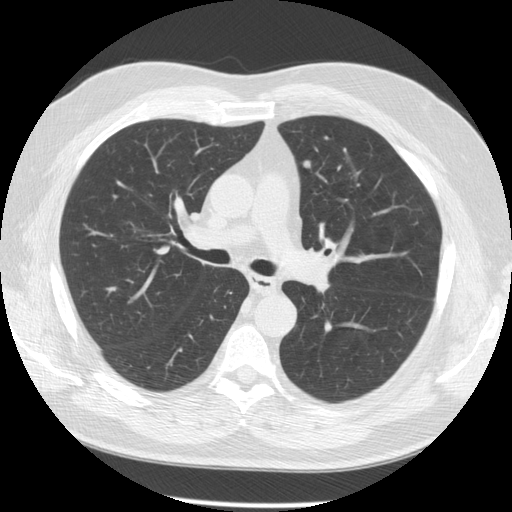
Low-dose screening chest CT, one axial slice; position 87 of 137 along the scan axis; reconstruction kernel STANDARD; 120 kVp; lung window (W 1500 / L -600 HU); 2.5 mm slice thickness; 512 × 512 image matrix, field of view 370 × 370 mm.
Outlined on this slice (expert manual segmentation):
- lesion 1 (tumor, upper lobe of left lung): bounding box [x1, y1, x2, y2] px = [303, 160, 311, 168]